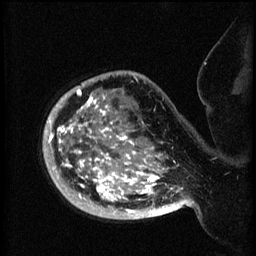
Breast MRI (dynamic contrast-enhanced), one sagittal slice; slice 52 of 60 in the series (ordered by position); 3 images stored at this slice position (order not interpretable as contrast timing); 1.5 T; TE 4.2 ms, TR 8.2 ms; 2 mm slice thickness; 256 × 256 image matrix. Female patient, age 50 years.
Outlined on this slice (semi-automatic segmentation, software-assisted and operator-edited):
- analysis volume of interest (the breast-tissue region the enhancement analysis was run in; not a lesion): box from (x=44, y=72) to (x=173, y=219) px
- tumour enhancement mask (voxels above the 70 % enhancement threshold inside the analysis volume of interest): (x=45, y=90)–(x=173, y=215)